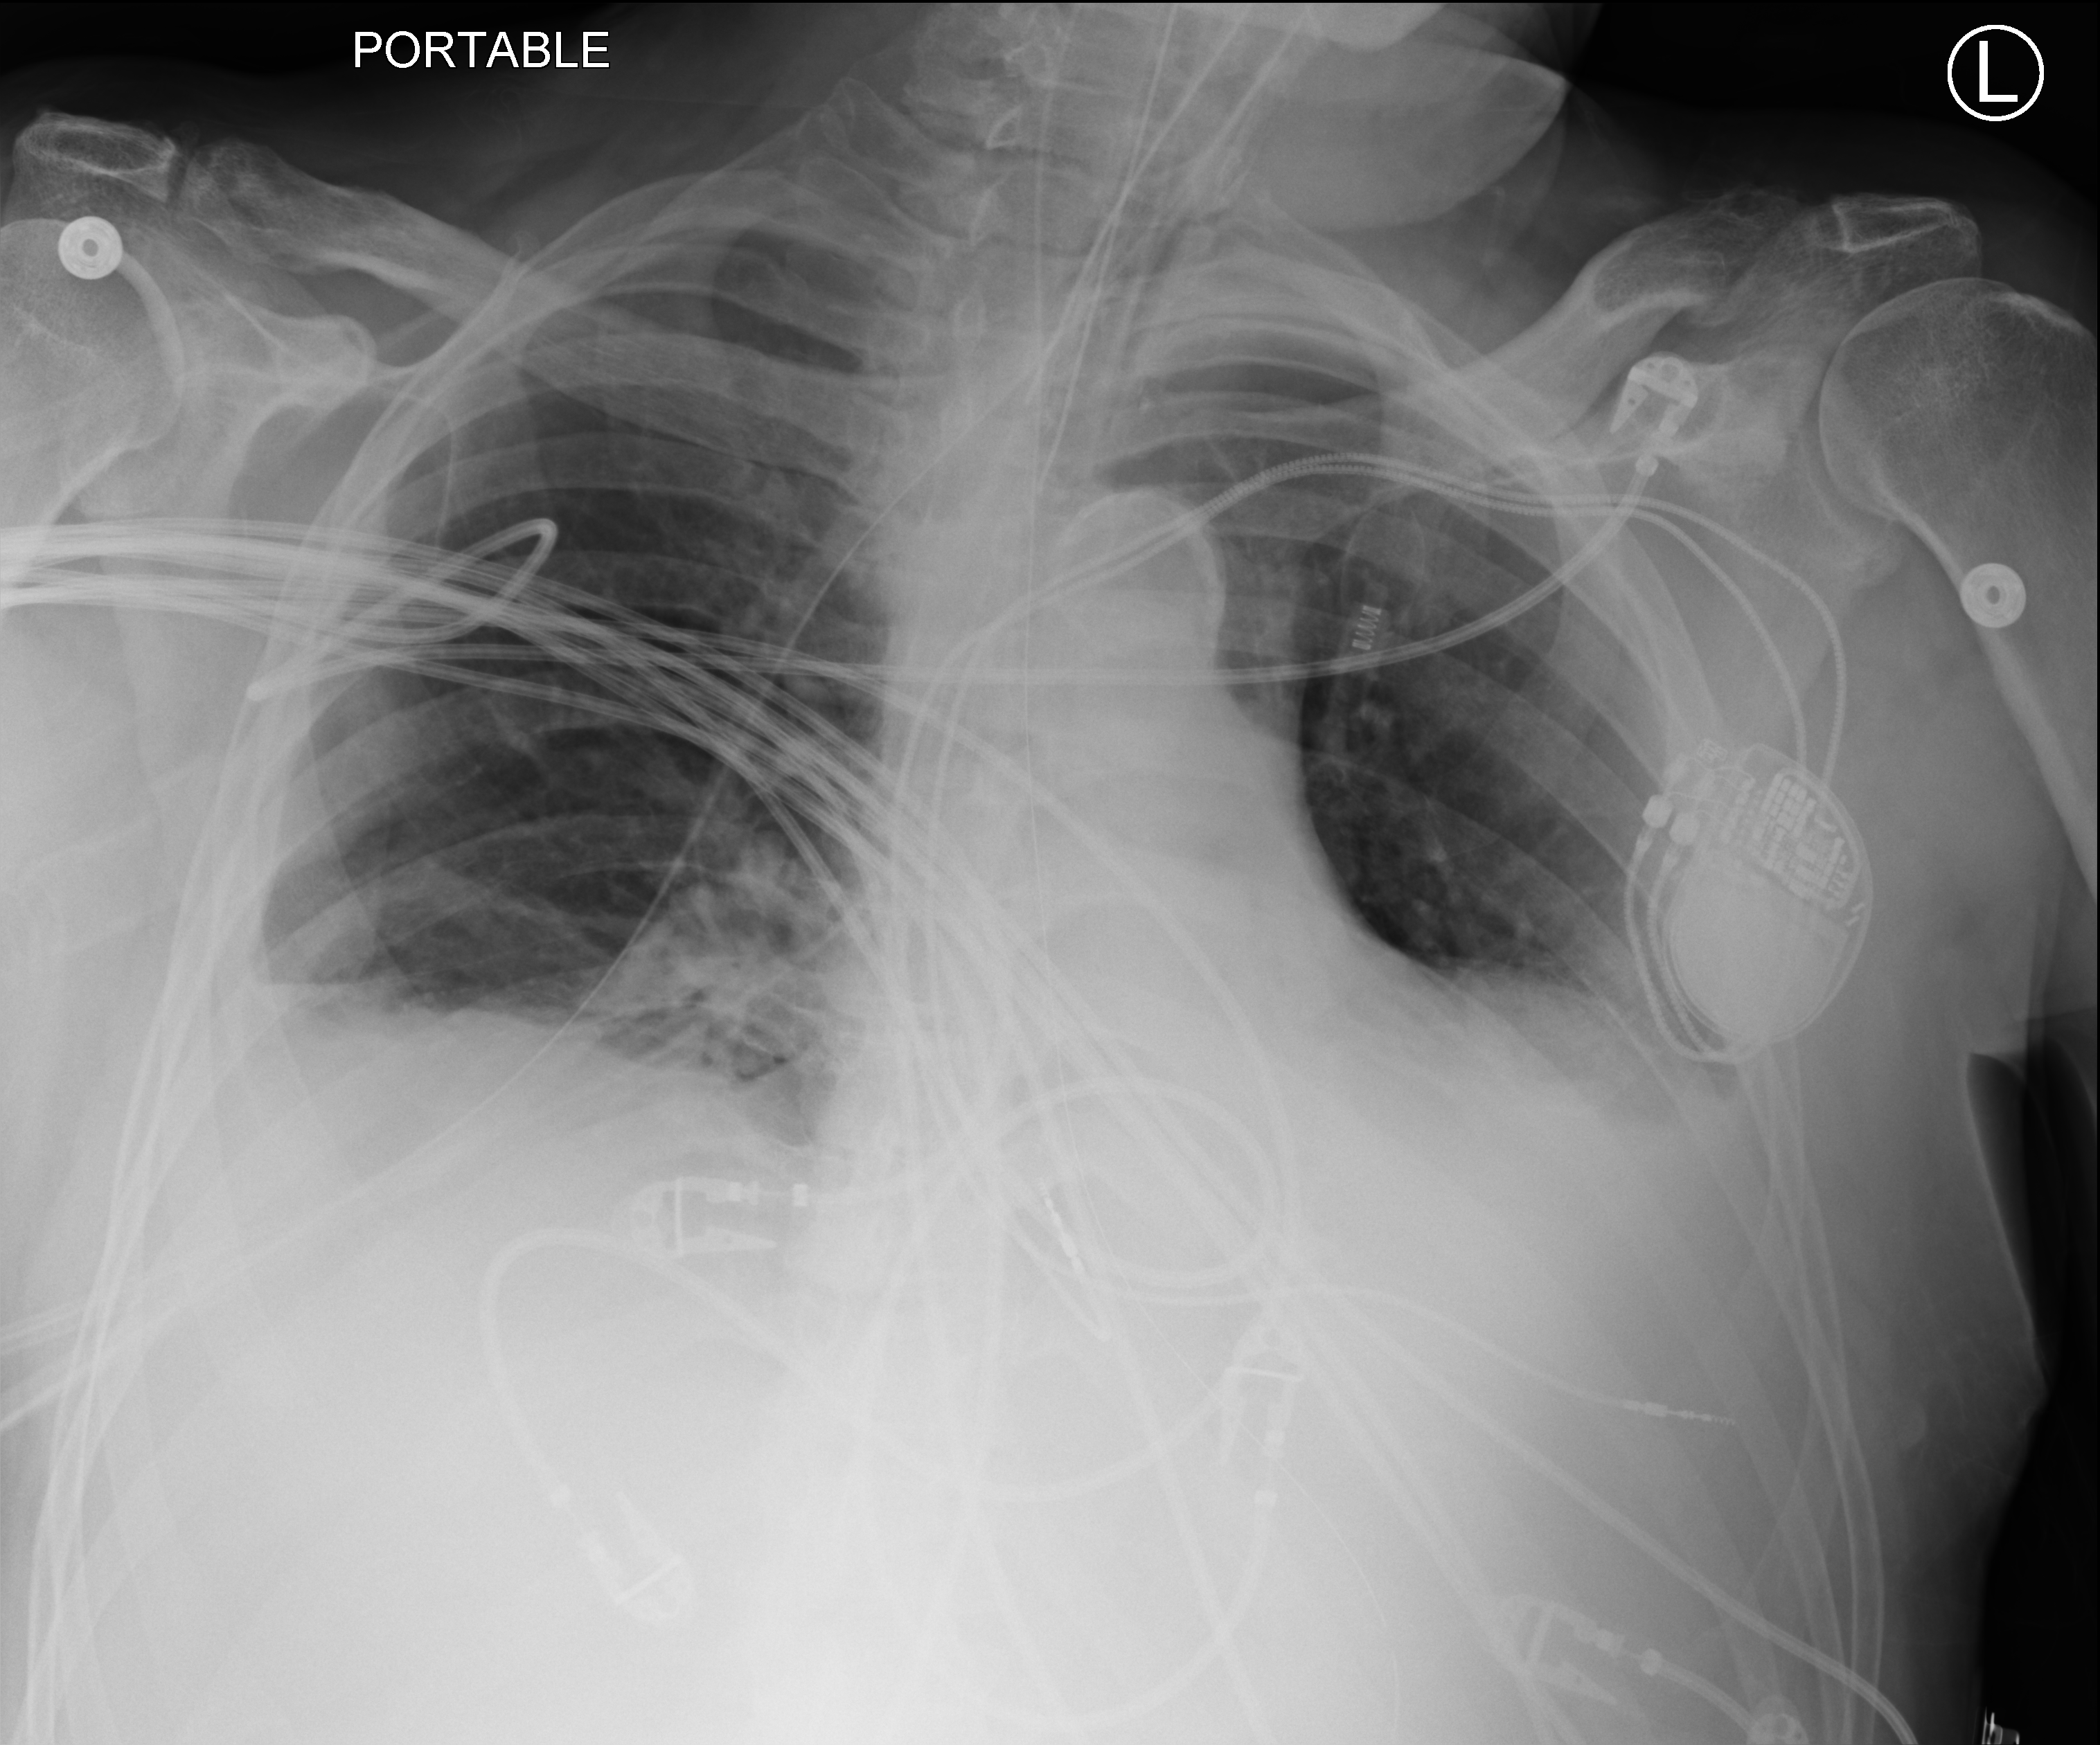
Portable chest radiograph, anteroposterior (AP) projection. Patient hospitalised with COVID-19; male, aged 60–74 years.
Hospital-stay facts (about this admission, not read from this image; timing relative to this image not recorded): admitted to intensive care during this hospital stay: yes.